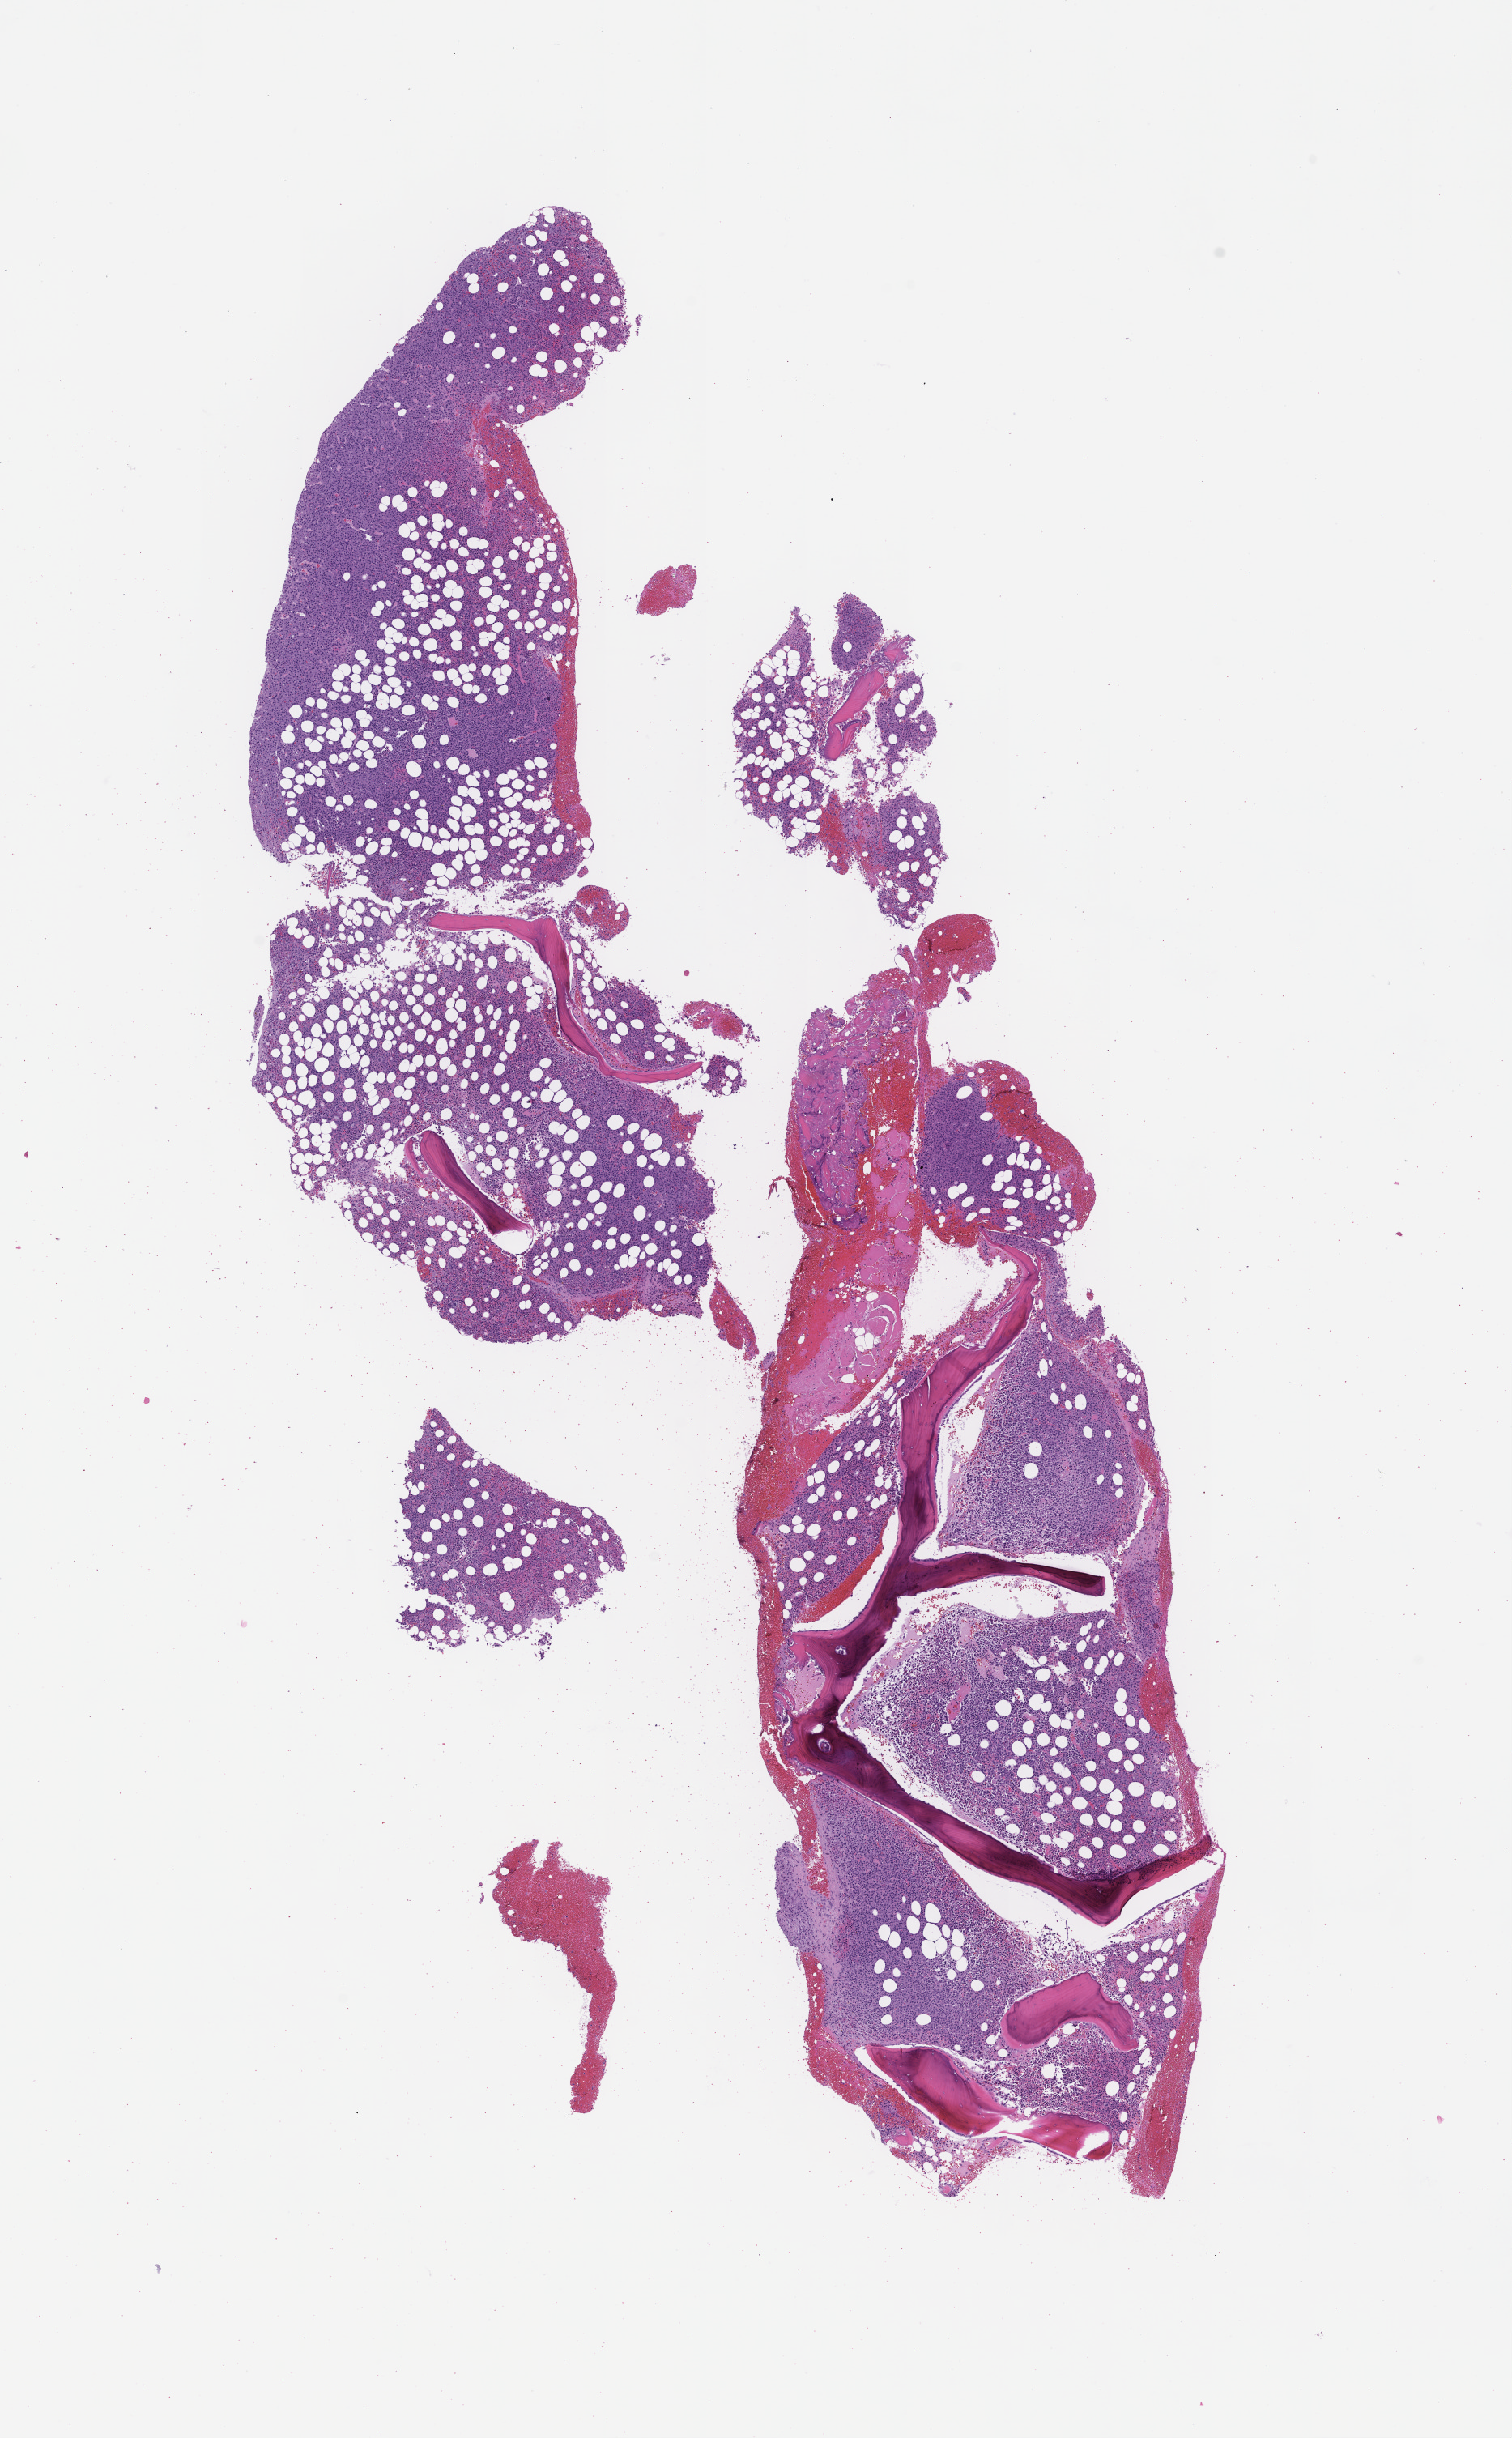
Haematoxylin and eosin whole-slide image — whole scanned area (about 7.5 x 12.2 mm) shown as a low-resolution overview, formalin-fixed, paraffin-embedded (FFPE) tissue, site: bone marrow, archival tissue. Patient sex: male.
This section: primary tumour tissue. Diagnosis: Plasma Cell Myeloma.